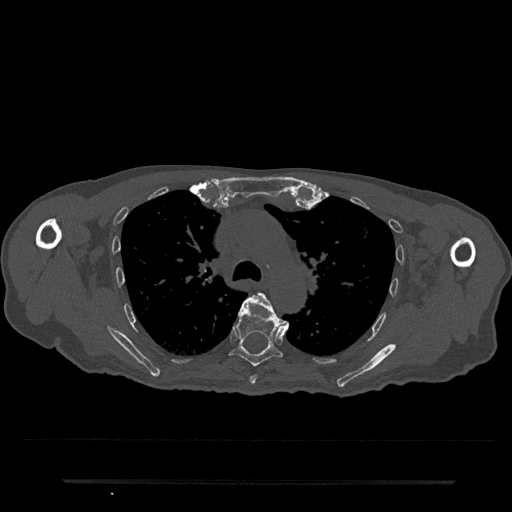
CT including the spine, one axial slice. 120 kVp. Bone window (W 1800 / L 400 HU). 0.5 mm slice thickness. 512 × 512 image matrix. Patient: male, 74 years. From the clinical record (not read from this slice): primary cancer: prostate.
Structures marked on this image (semi-automatic segmentation, software-assisted and operator-edited):
- T5 vertebra: bounding box (x1, y1, x2, y2) in pixels: (240, 293, 289, 385)
- T6 vertebra: (229, 298, 282, 367)